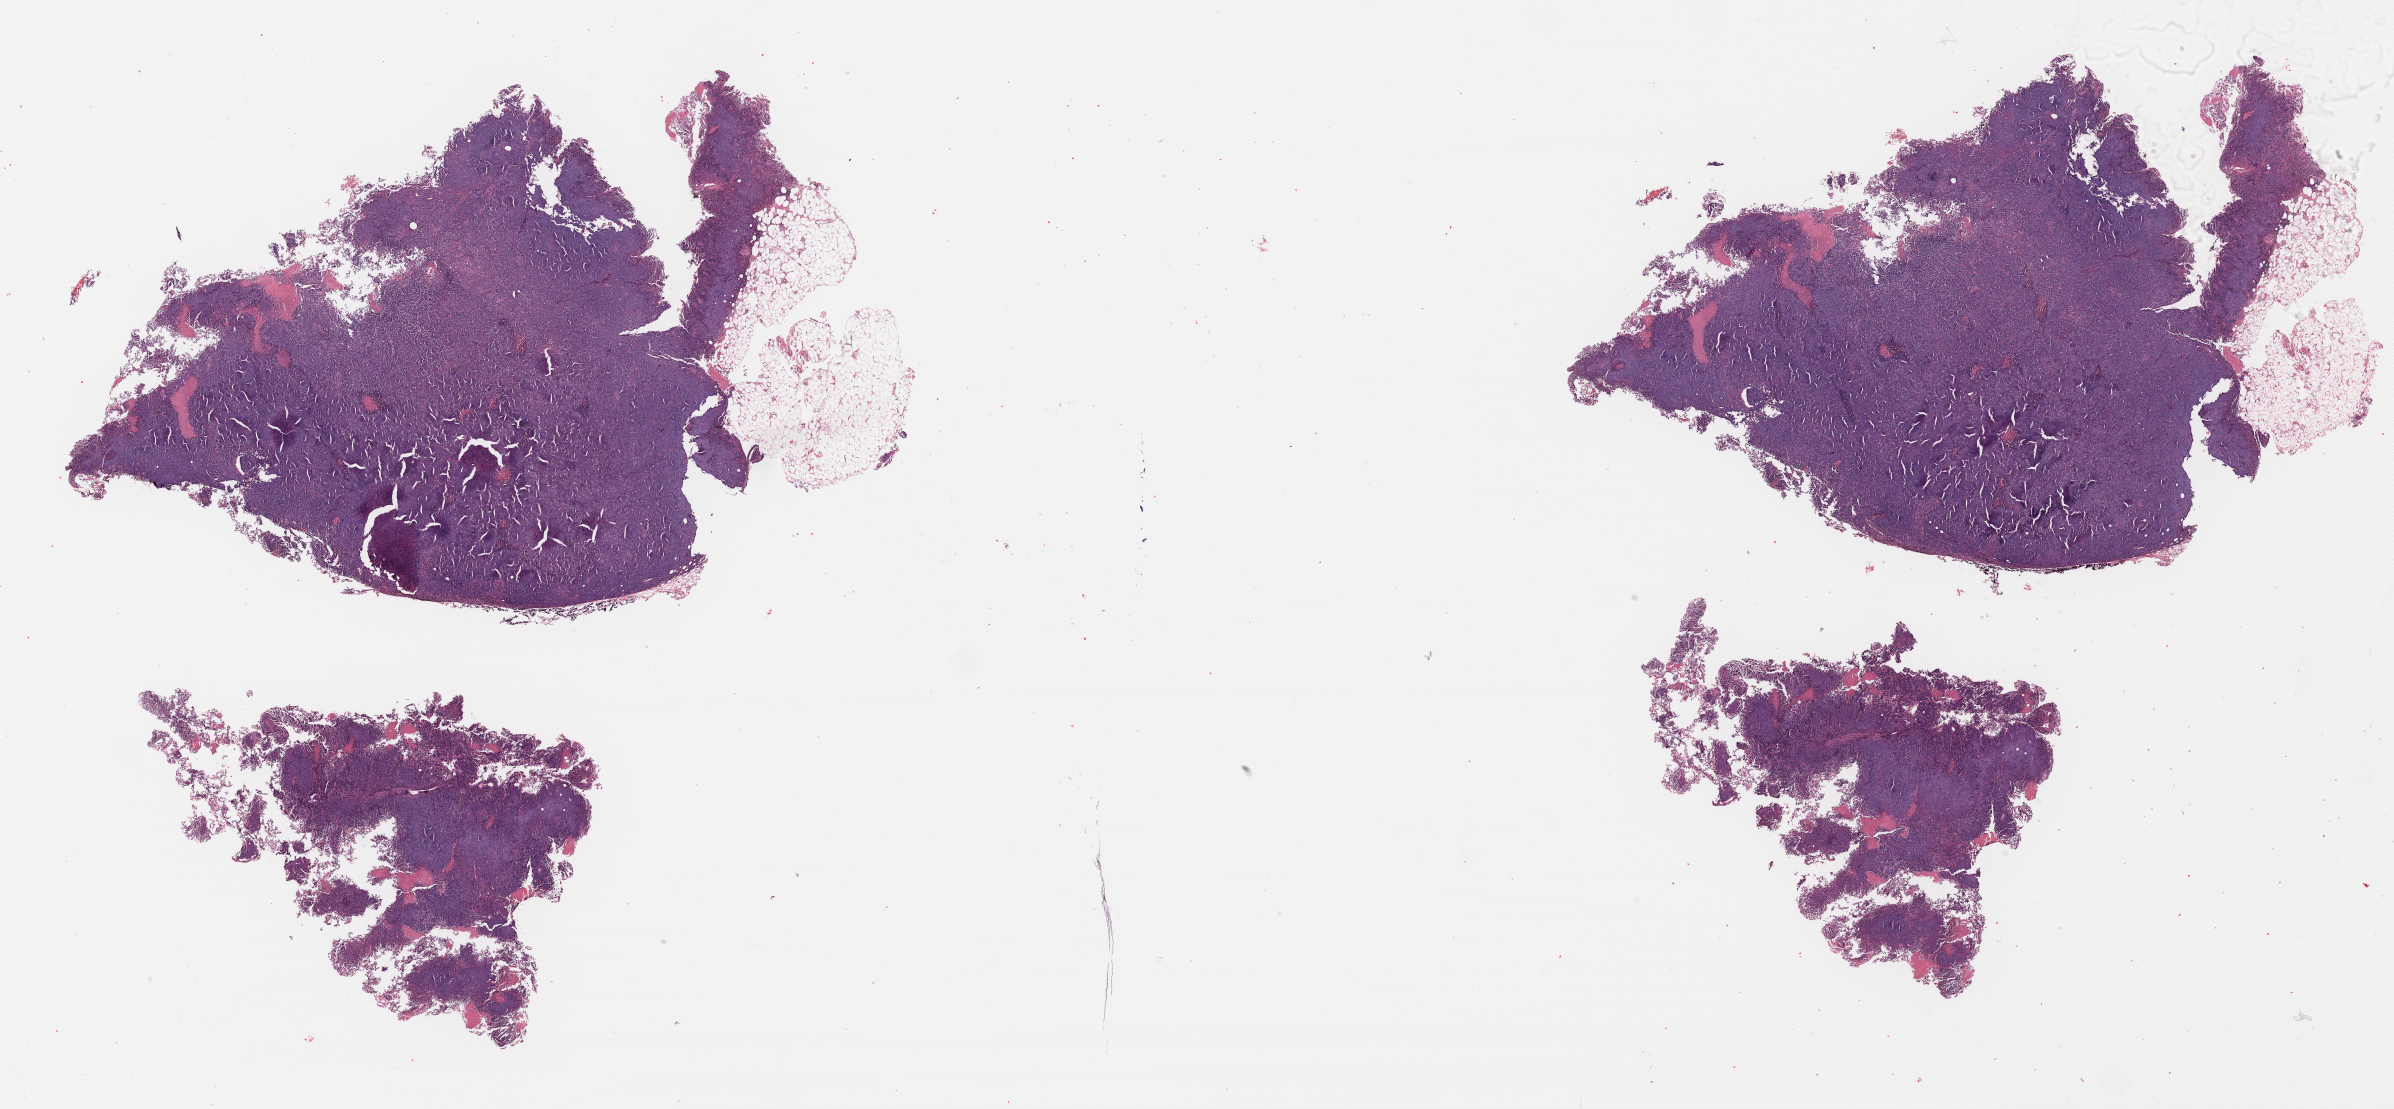
Digitized Hematoxylin and eosin (H&E) stained tissue section (whole slide) — shown as a low-resolution overview of the whole scanned area (about 37.6 x 17.4 mm, from a 40x scan). FFPE section. Metastatic tumour sample, sampled site: lymph node. Female, age 45 years at initial diagnosis.
* this section: metastatic tumour tissue
* patient diagnosis: Malignant melanoma, NOS